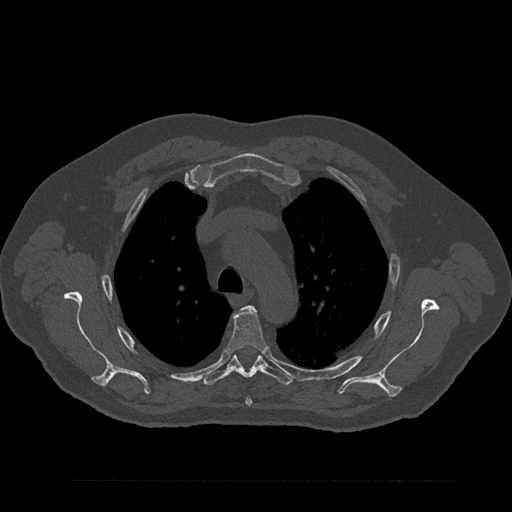
CT including the spine, one axial slice; position 627 of 797 along the scan axis; 120 kVp; bone window (W 1800 / L 400 HU); 0.5 mm slice thickness; 512 × 512 image matrix, field of view 430 × 430 mm. Patient: male, 61 years. From the clinical record (not read from this slice): primary cancer: prostate.
Structures marked on this image (semi-automatic segmentation, software-assisted and operator-edited):
- T3 vertebra: bounding box [x1, y1, x2, y2] px = [243, 306, 254, 308]
- T4 vertebra: [228, 306, 268, 406]
- T5 vertebra: [203, 355, 292, 386]